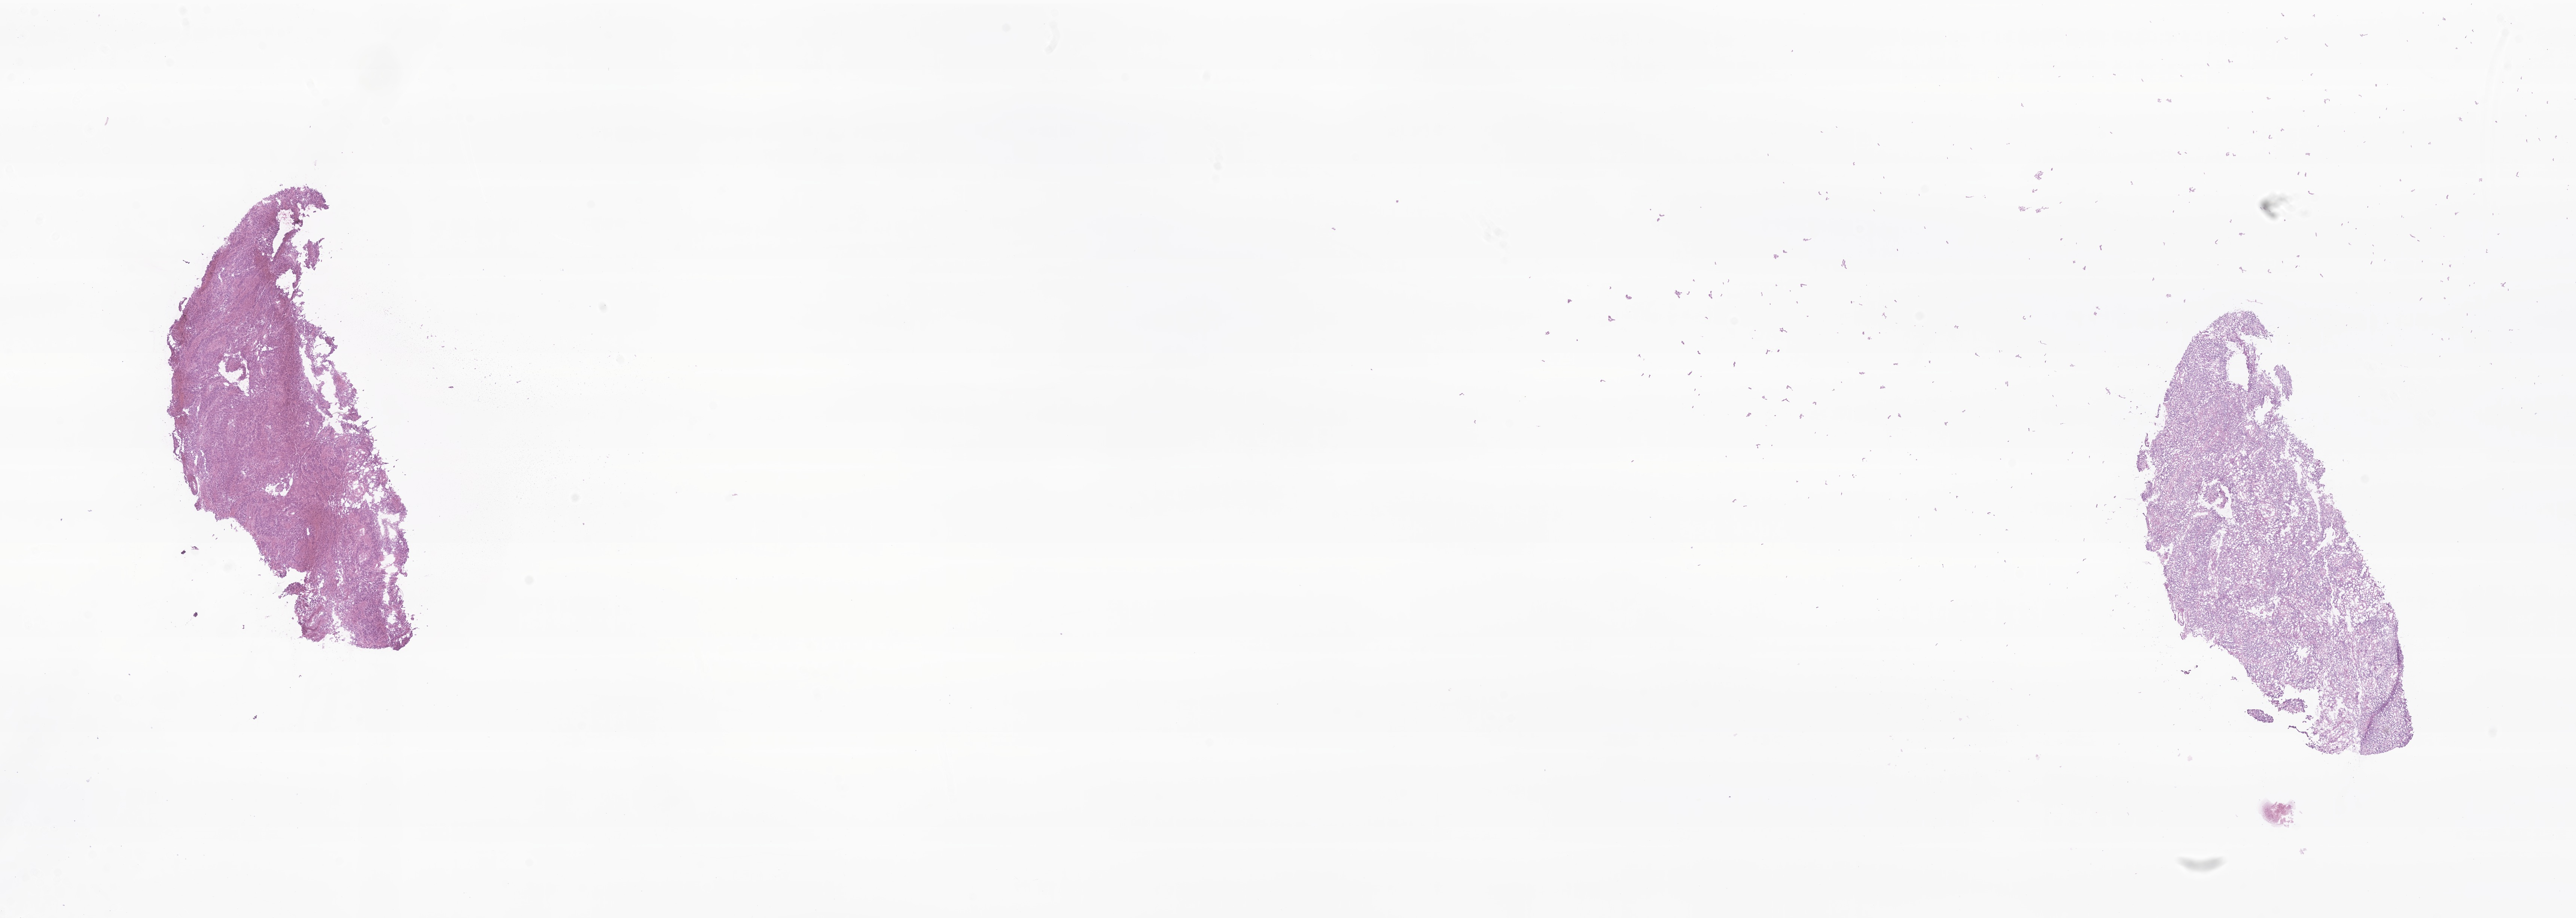
Whole-slide image, H&E stain of tumor tissue from the brain, a low-resolution overview of the entire scanned area, about 29.0 x 10.3 mm; frozen section. Male patient, age 132 months.
Diagnosis: Neoplasm, malignant.